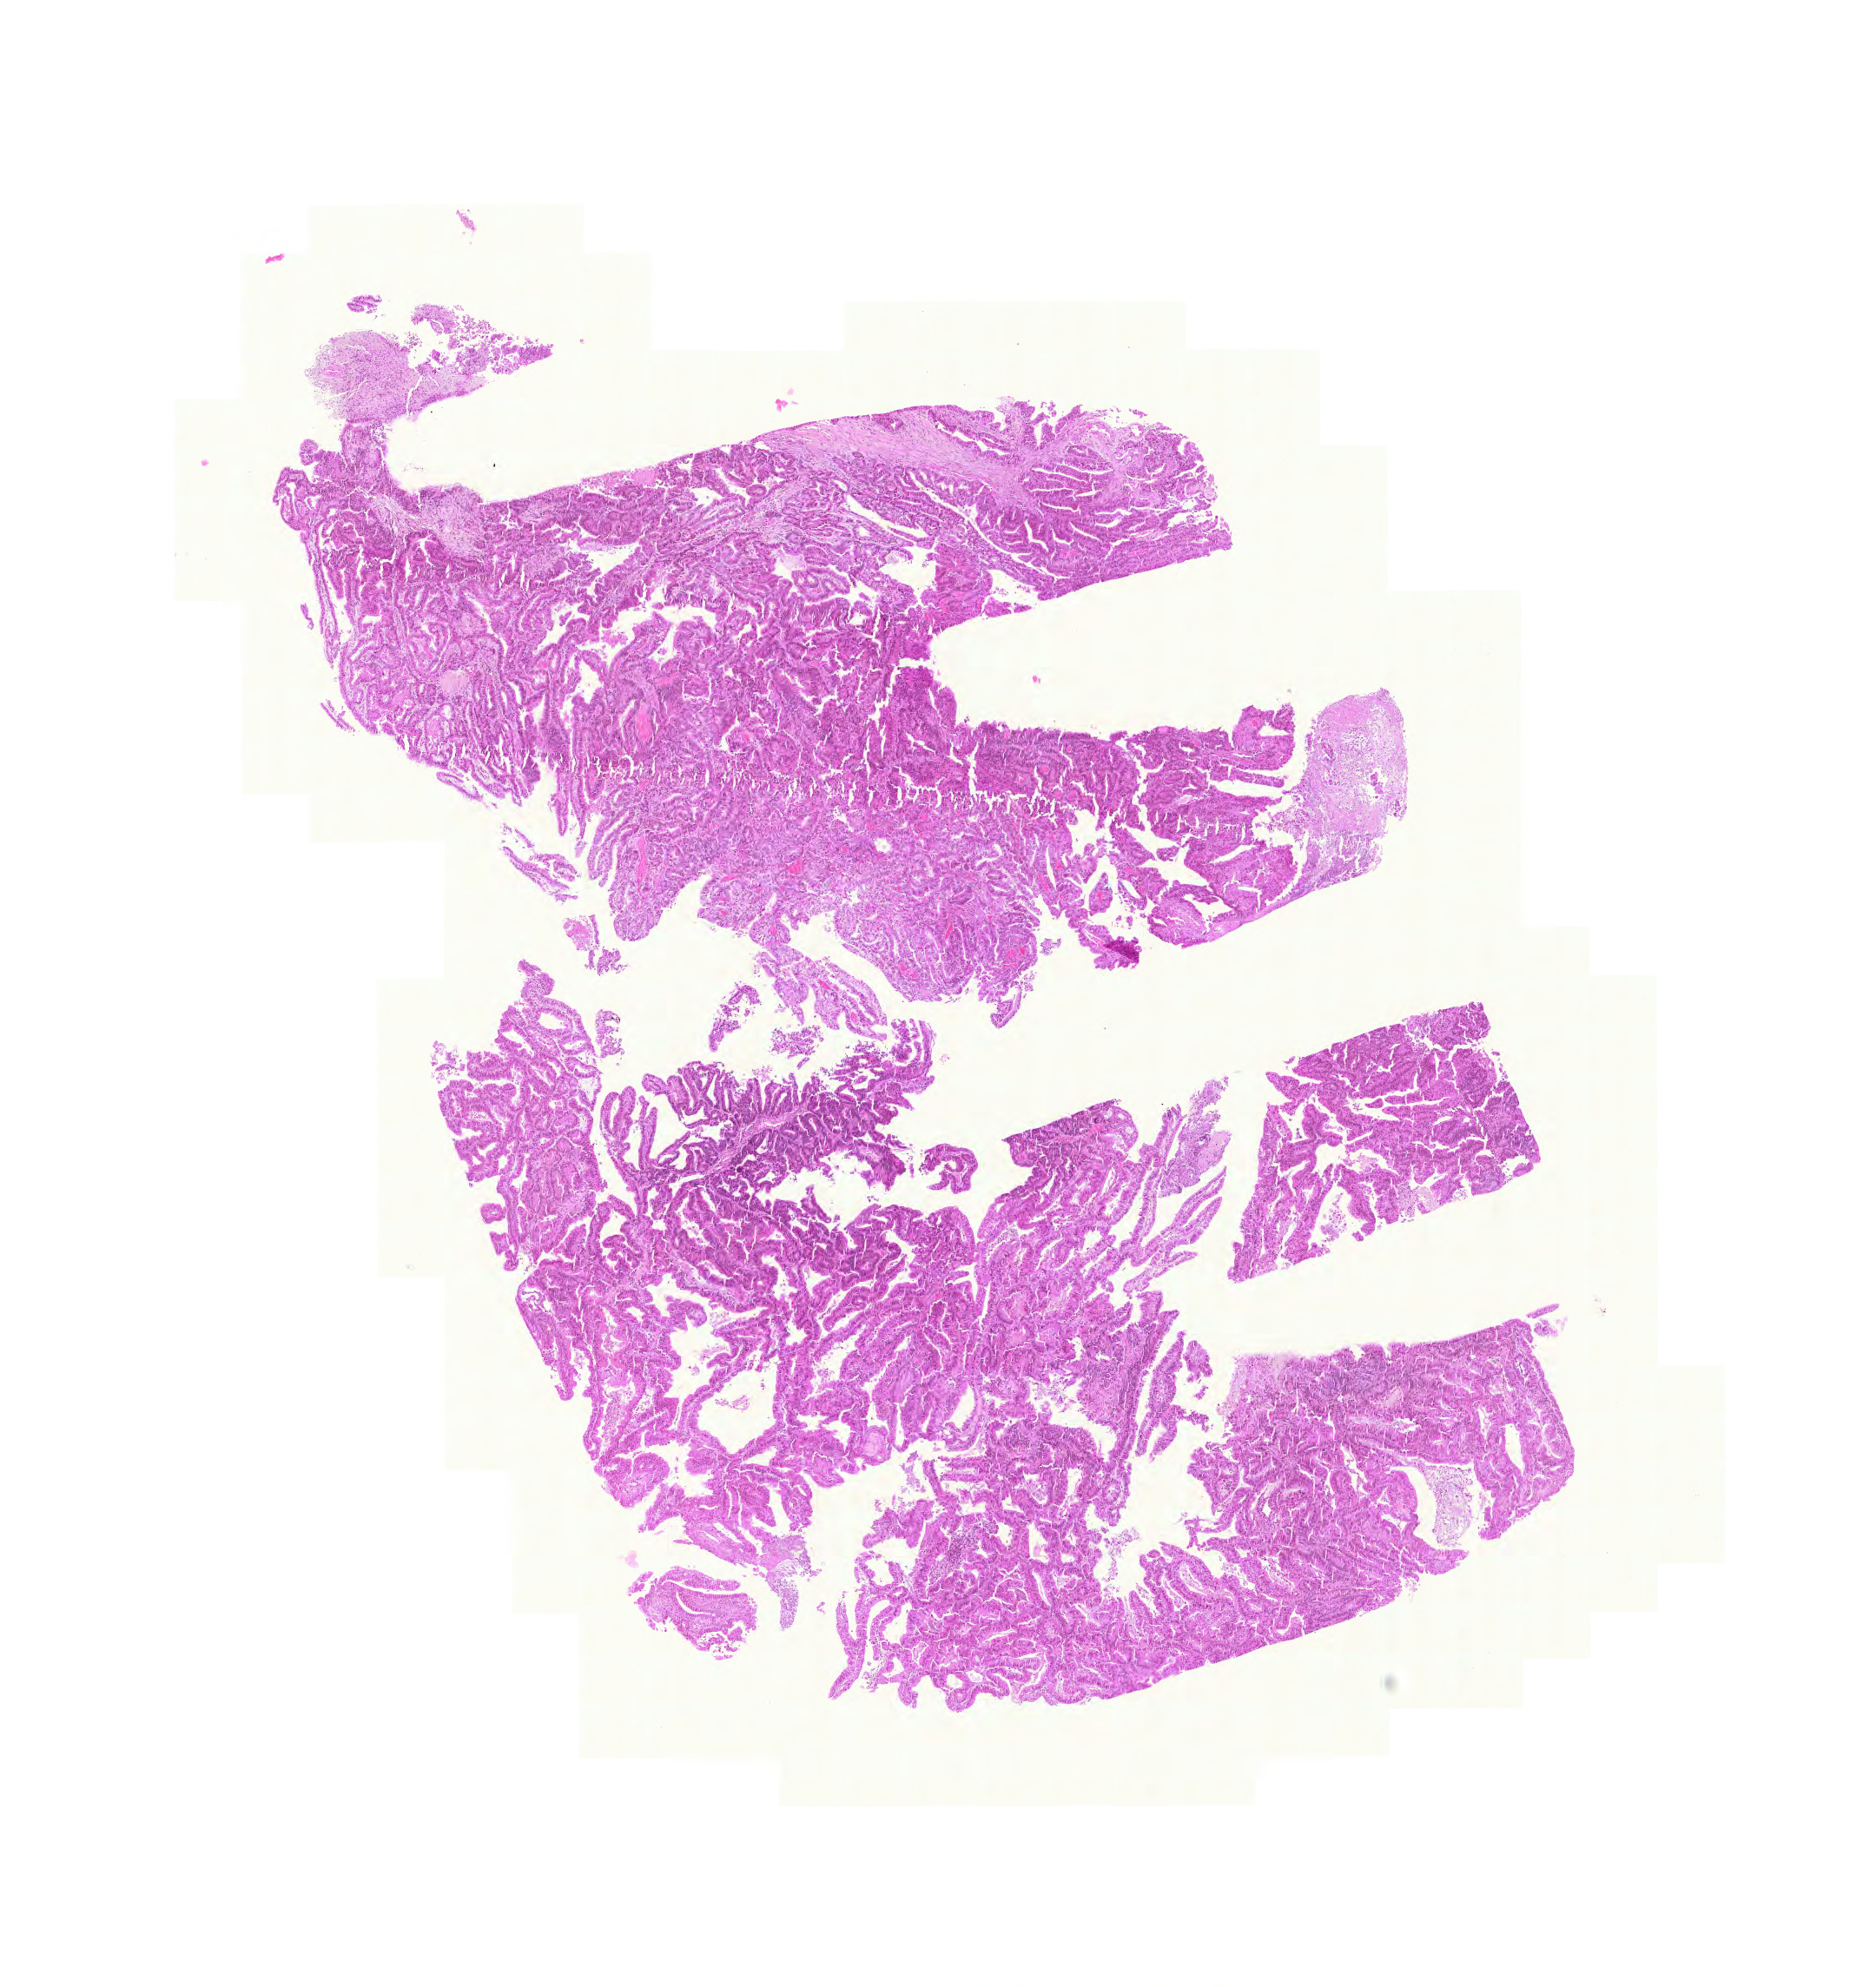
Digitized Hematoxylin and eosin (H&E) stained tissue section (whole slide), a low-resolution overview of the entire scanned area, about 8.0 x 8.5 mm; formalin-fixed paraffin-embedded (FFPE) diagnostic section; primary tumour sample from the stomach. Male patient; age at initial diagnosis 83 years. Histologic grade: G2 (moderately differentiated).
Histologic diagnosis: Adenocarcinoma, intestinal type (body of stomach). AJCC pathologic stage: IIIA.